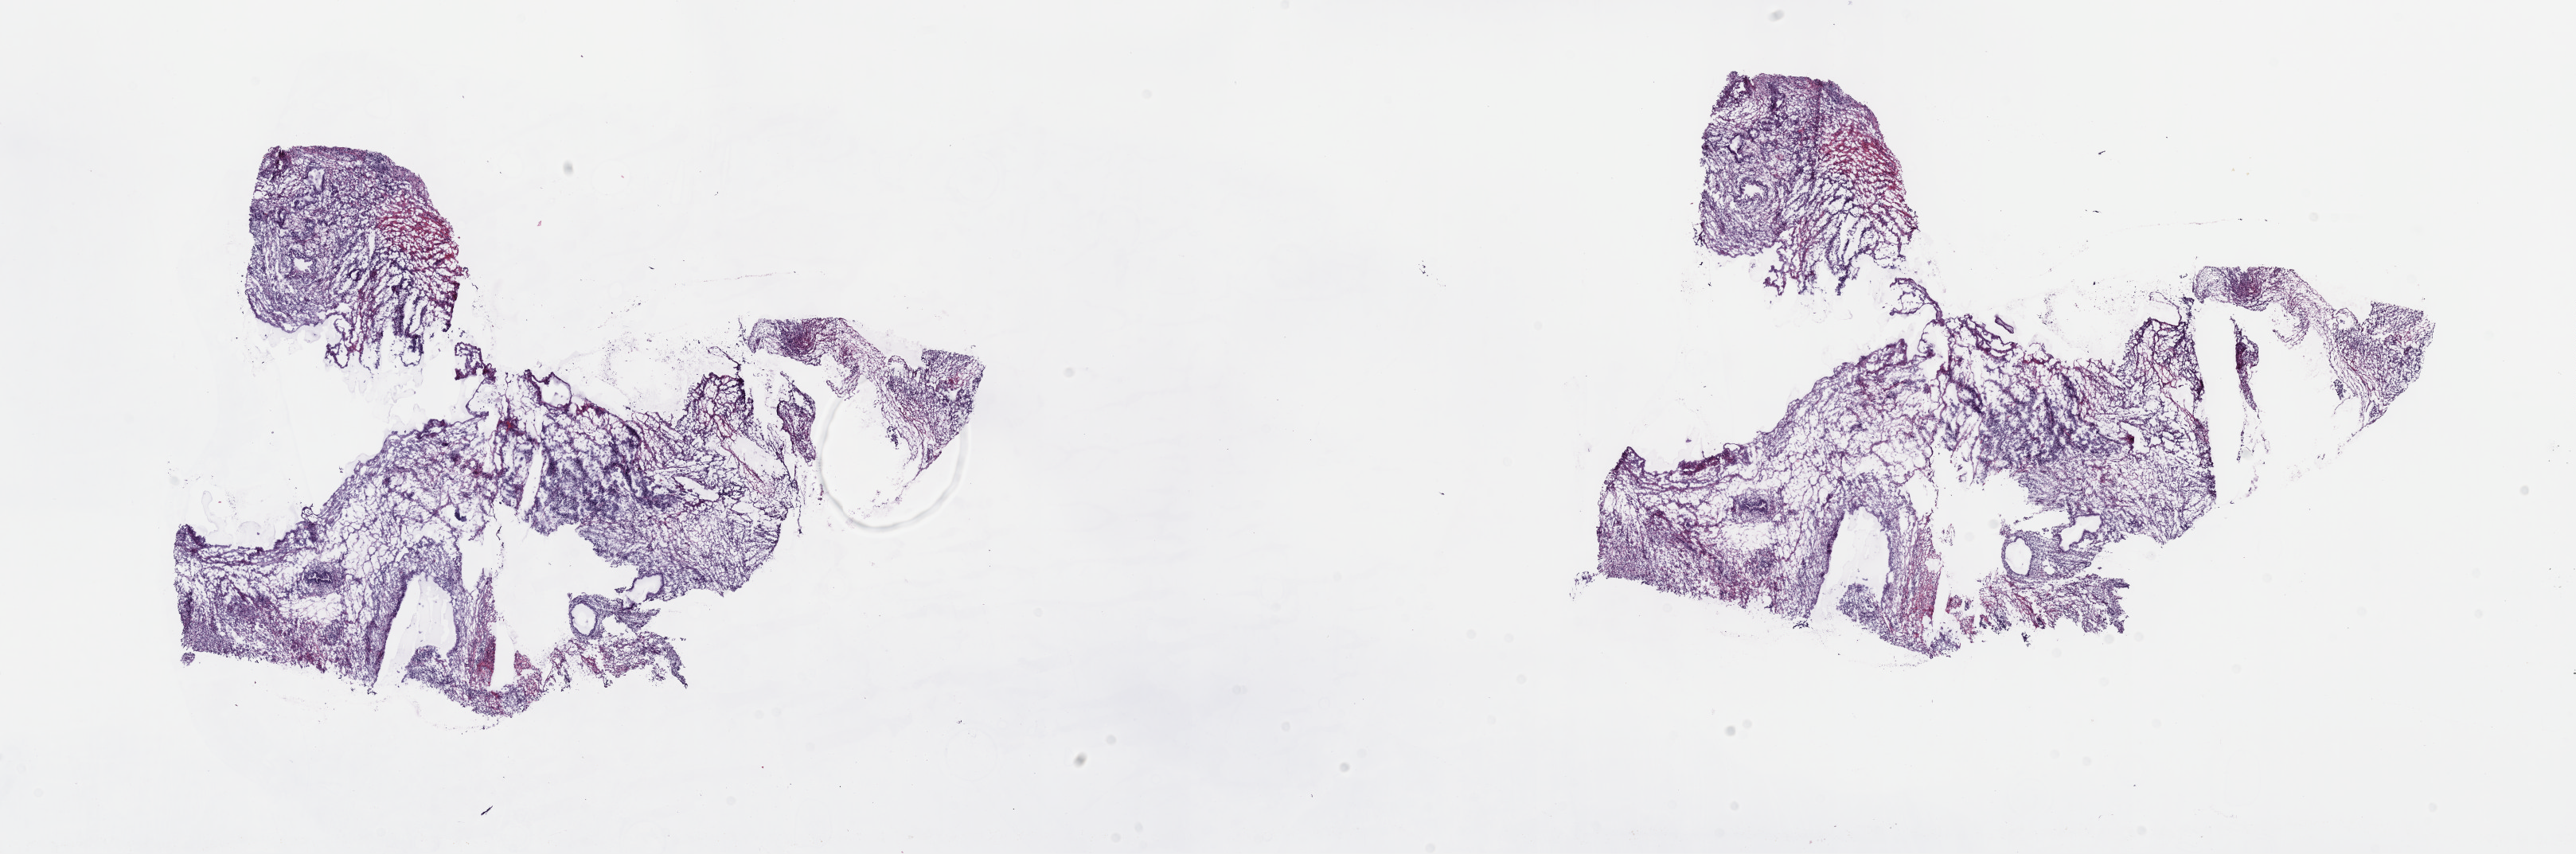
H&E-stained whole-slide image, shown as a low-resolution overview of the whole scanned area (about 26.2 x 8.7 mm, acquisition: 40x scan). Frozen section from the top of the tissue portion. Testis, primary tumour sample. Male, age 37 years at initial diagnosis. Slide review estimates, as recorded: tumour cells 100%, tumour nuclei 80%, normal cells 0%, stromal cells 0%, necrosis 0%. Infiltration values recorded for this section: lymphocyte infiltration 3%, monocyte infiltration 0%, neutrophil infiltration 0%.
Histologic diagnosis: Teratocarcinoma. AJCC pathologic stage: IS (6th edition).